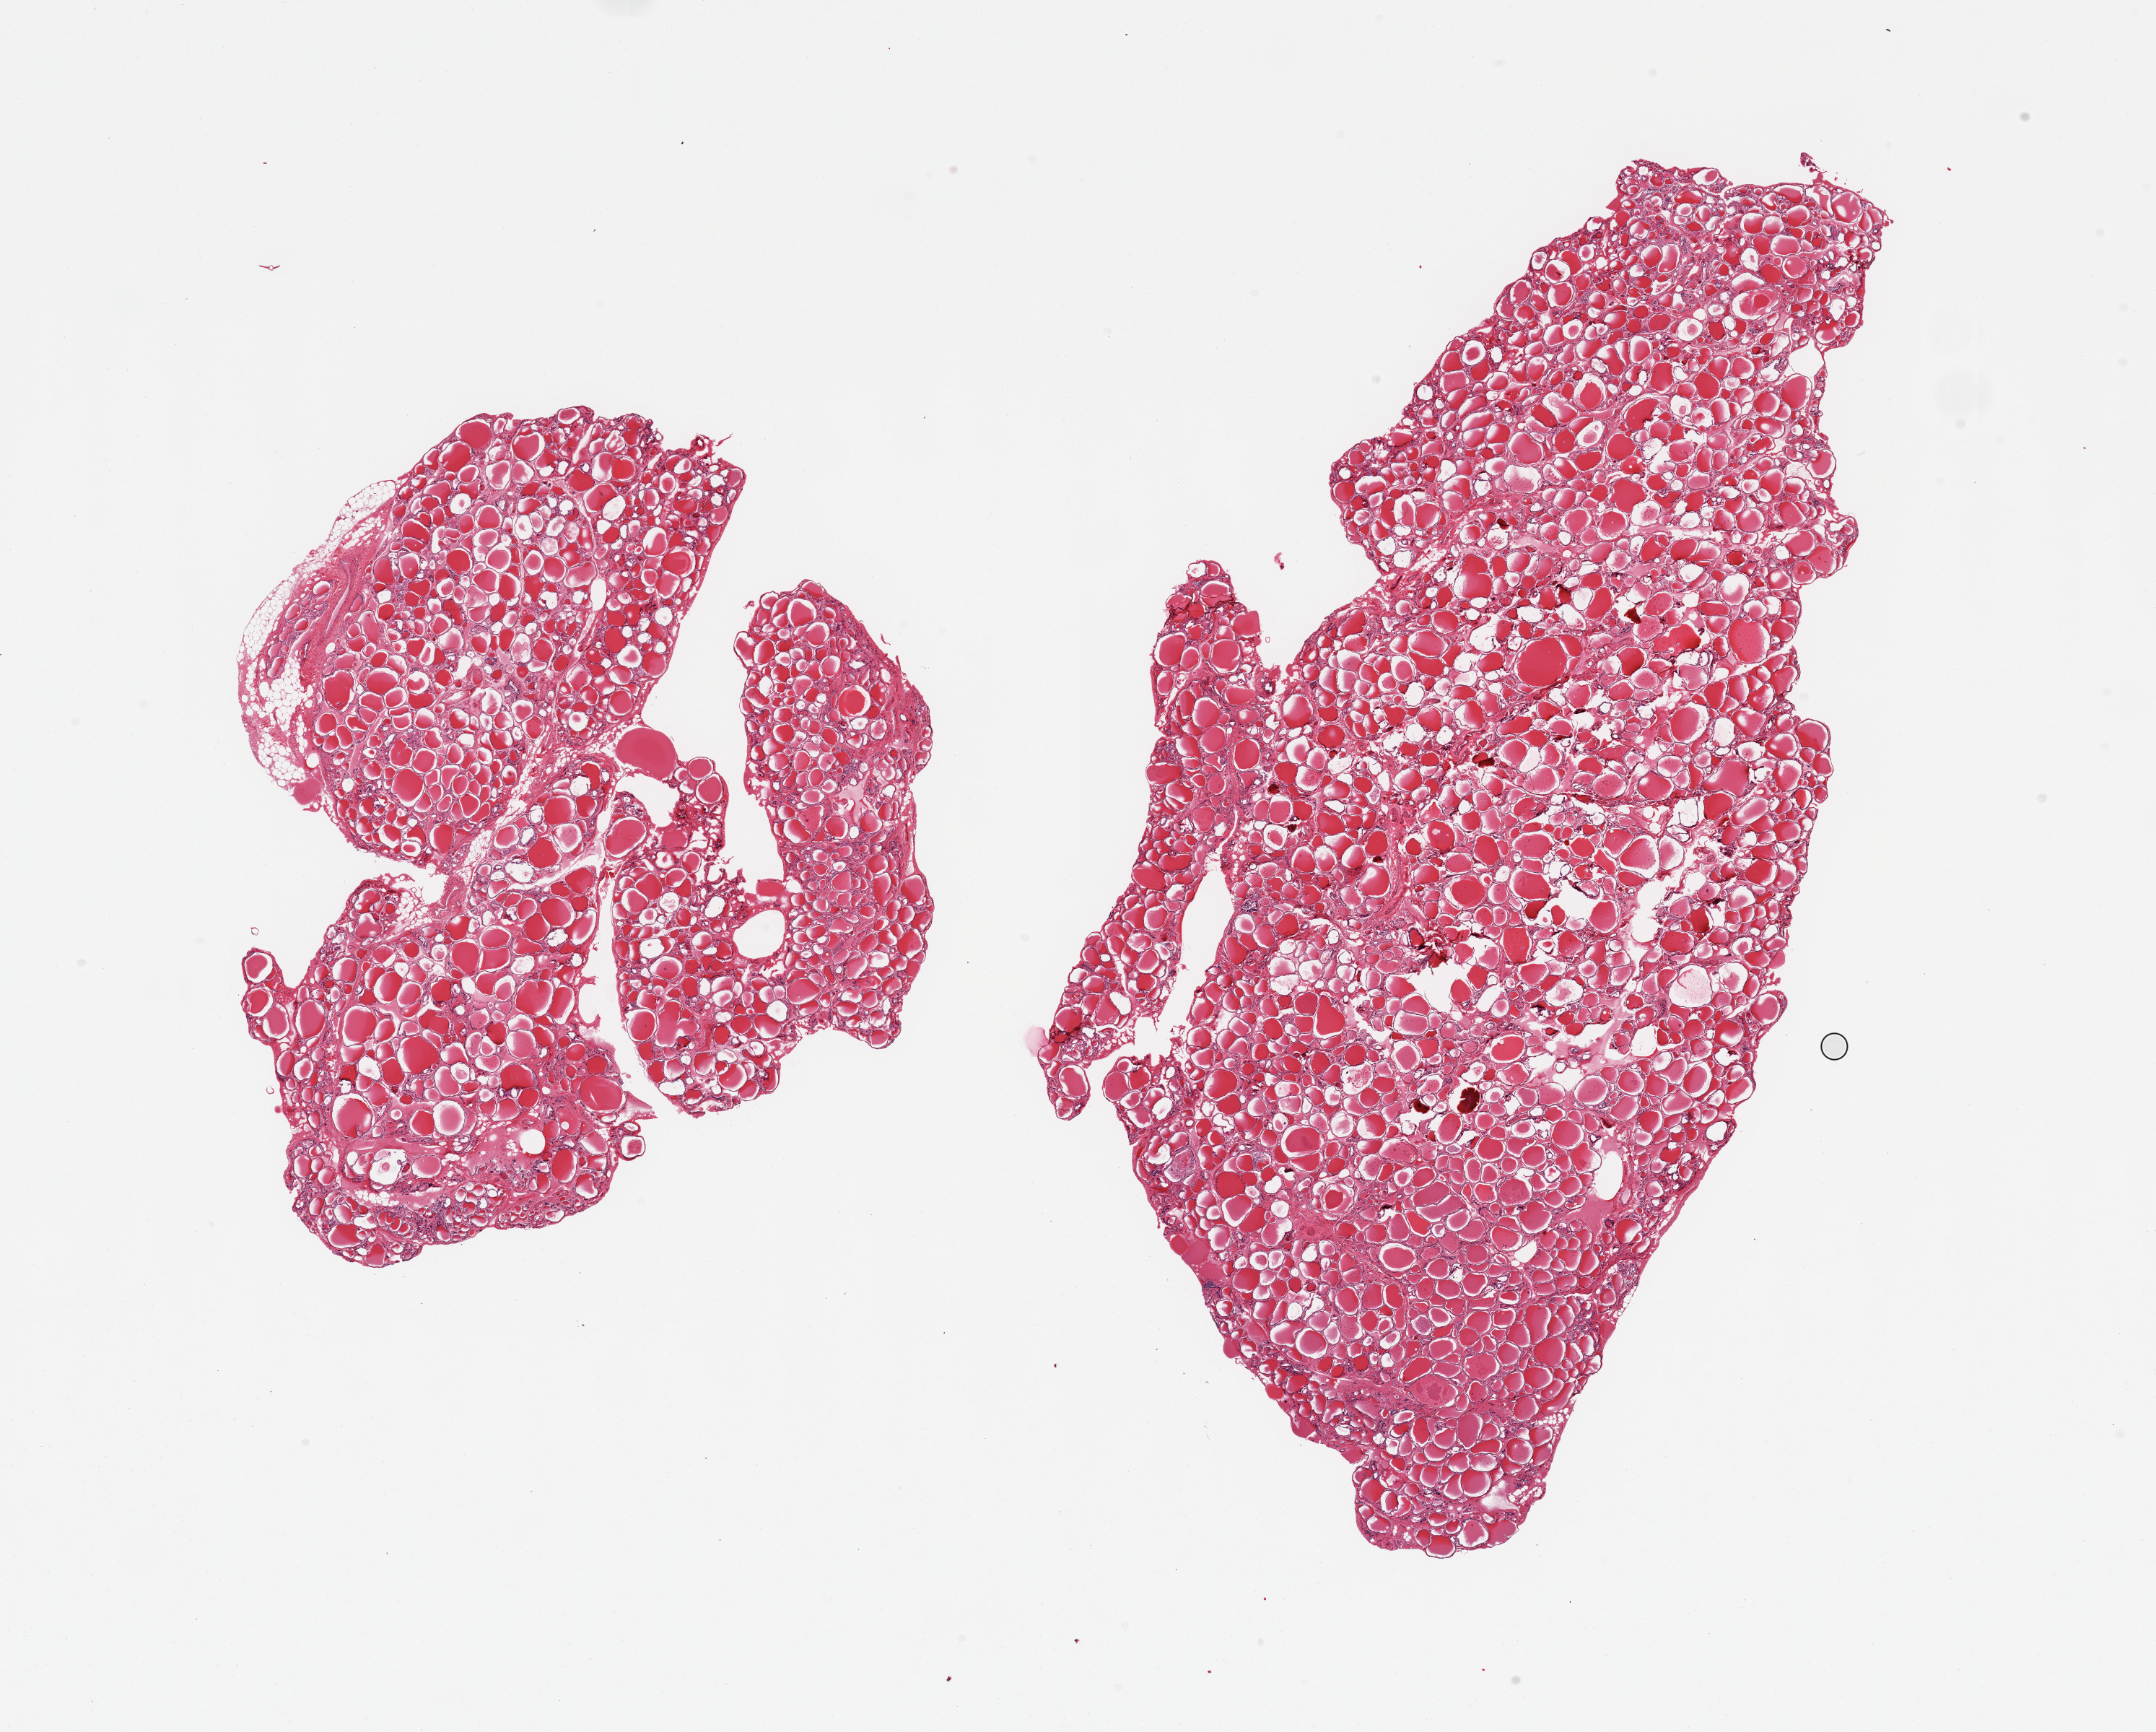
Hematoxylin and eosin (H&E) whole-slide image, brightfield — shown as a low-resolution overview of the whole scanned area (about 23.6 x 19.0 mm, acquisition: 20x scan), PAXgene-fixed paraffin-embedded (PFPE) section, target tissue: thyroid, tissue donor sample. Donor sex: male.
- pathologist's review note for this sample: 2 pieces; no pathologic changes noted